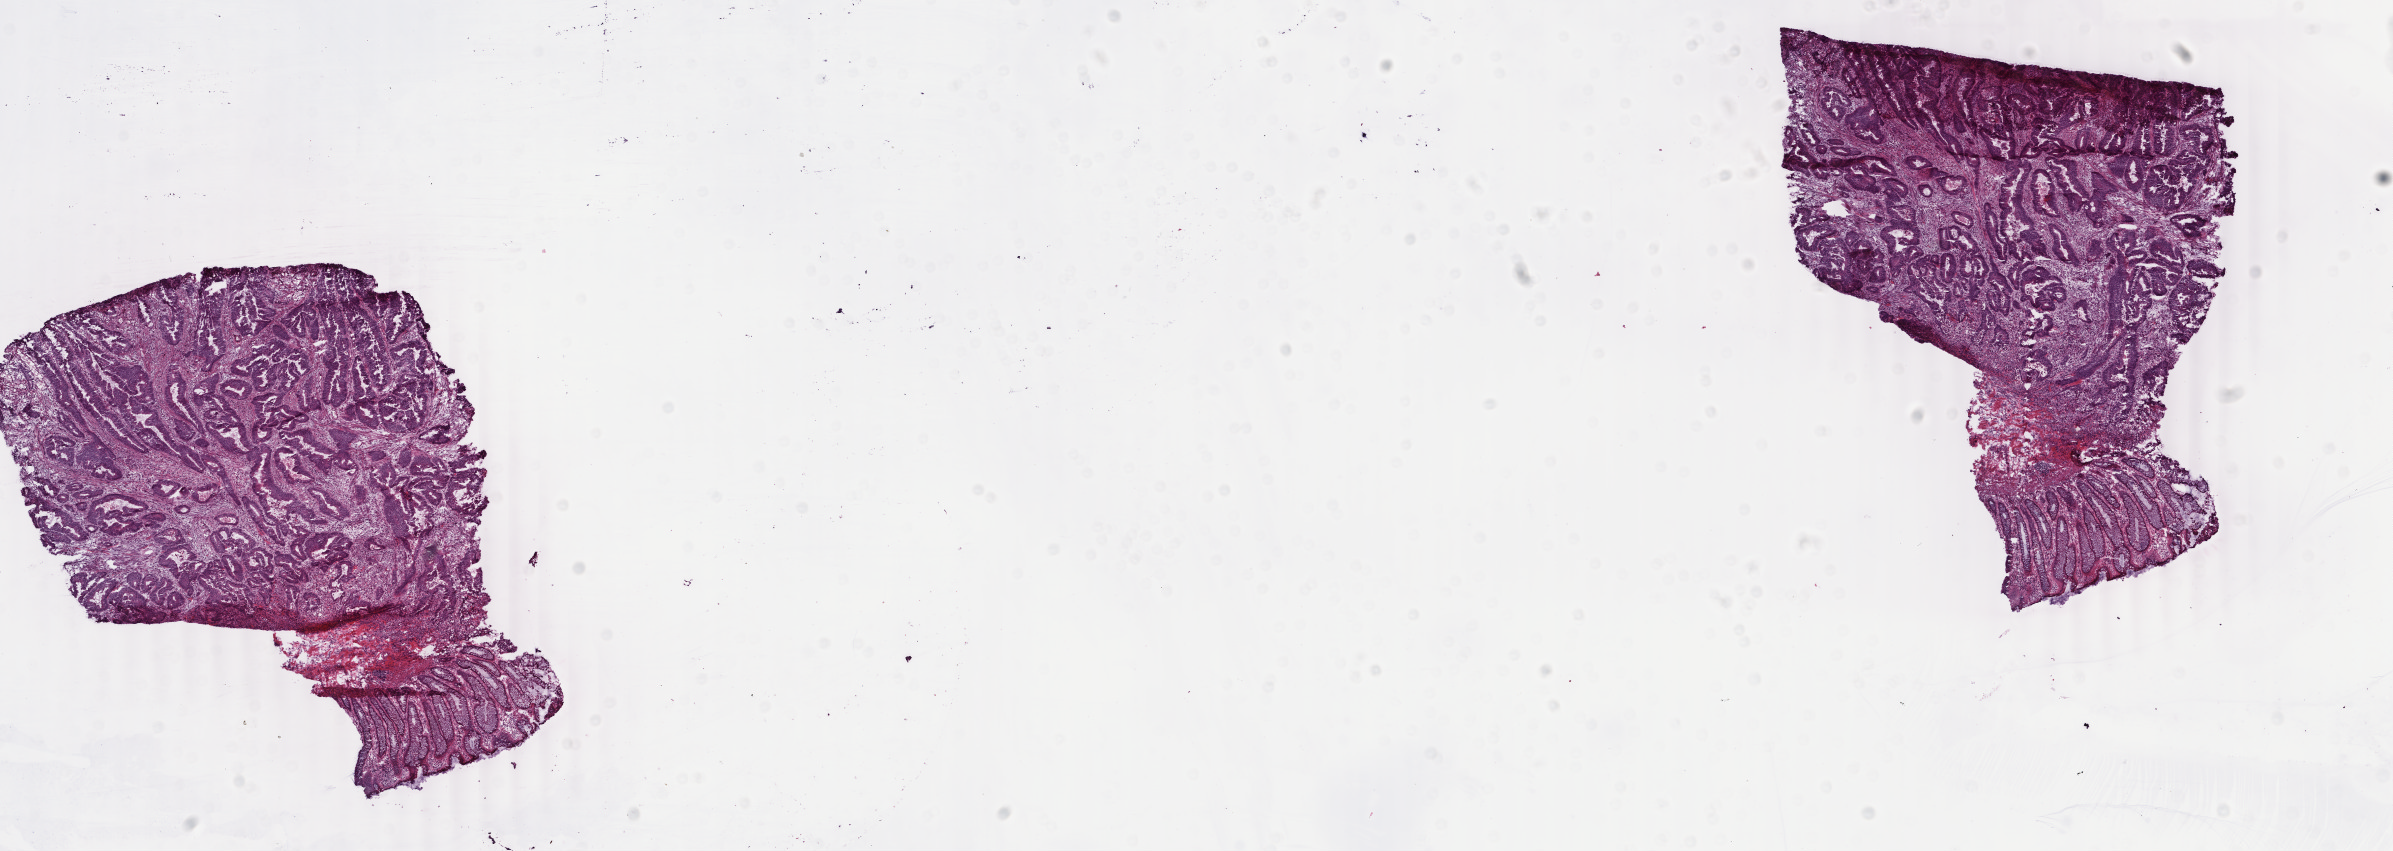
Whole-slide histology image, H&E-stained — low-resolution overview of the scanned area, about 19.0 x 6.8 mm (acquisition: 40x scan), frozen section, colon, primary tumour sample. Female patient; age at initial diagnosis 63 years. Pathologist review of this section (percent, as recorded): tumour cells 80%, tumour nuclei 80%, normal cells 5%, stromal cells 9%, necrosis 1%. Inflammatory infiltration, as recorded: lymphocyte infiltration 2%, monocyte infiltration 1%, neutrophil infiltration 9%.
- histologic diagnosis: Adenocarcinoma, NOS (sigmoid colon)
- lymph nodes positive (case pathology): 1 of 15 examined
- AJCC pathologic stage: III (5th edition)